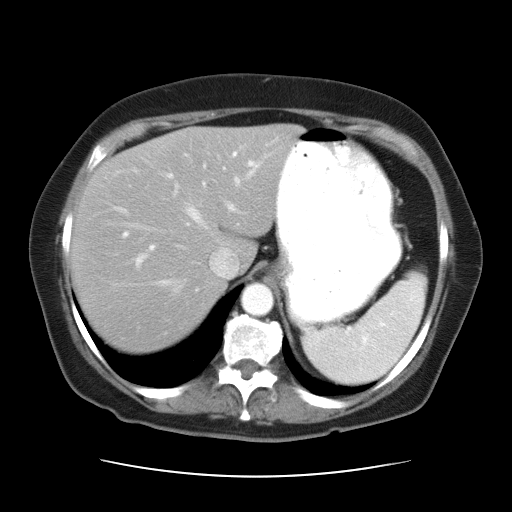
Contrast-enhanced abdominal CT, one axial slice. Position 25 of 34 along the scan axis. Reconstruction kernel STANDARD. Intravenous contrast given. Soft-tissue window (W 400 / L 40 HU). 512 × 512 image matrix. Female patient, age 65 years. From the clinical record (not read from this slice): diagnosis: colorectal cancer liver metastases, imaged before liver resection; multiple liver metastases: yes.
Outlined on this slice (outlined manually by an expert reader):
- hepatic veins: box from (x=112, y=159) to (x=260, y=292) px
- liver: (x=73, y=127)–(x=296, y=350)
- planned liver remnant (the part of the liver to remain after resection): (x=73, y=127)–(x=297, y=342)
- portal vein (with intrahepatic branches): (x=123, y=150)–(x=239, y=265)
- liver metastasis: (x=106, y=187)–(x=122, y=199)